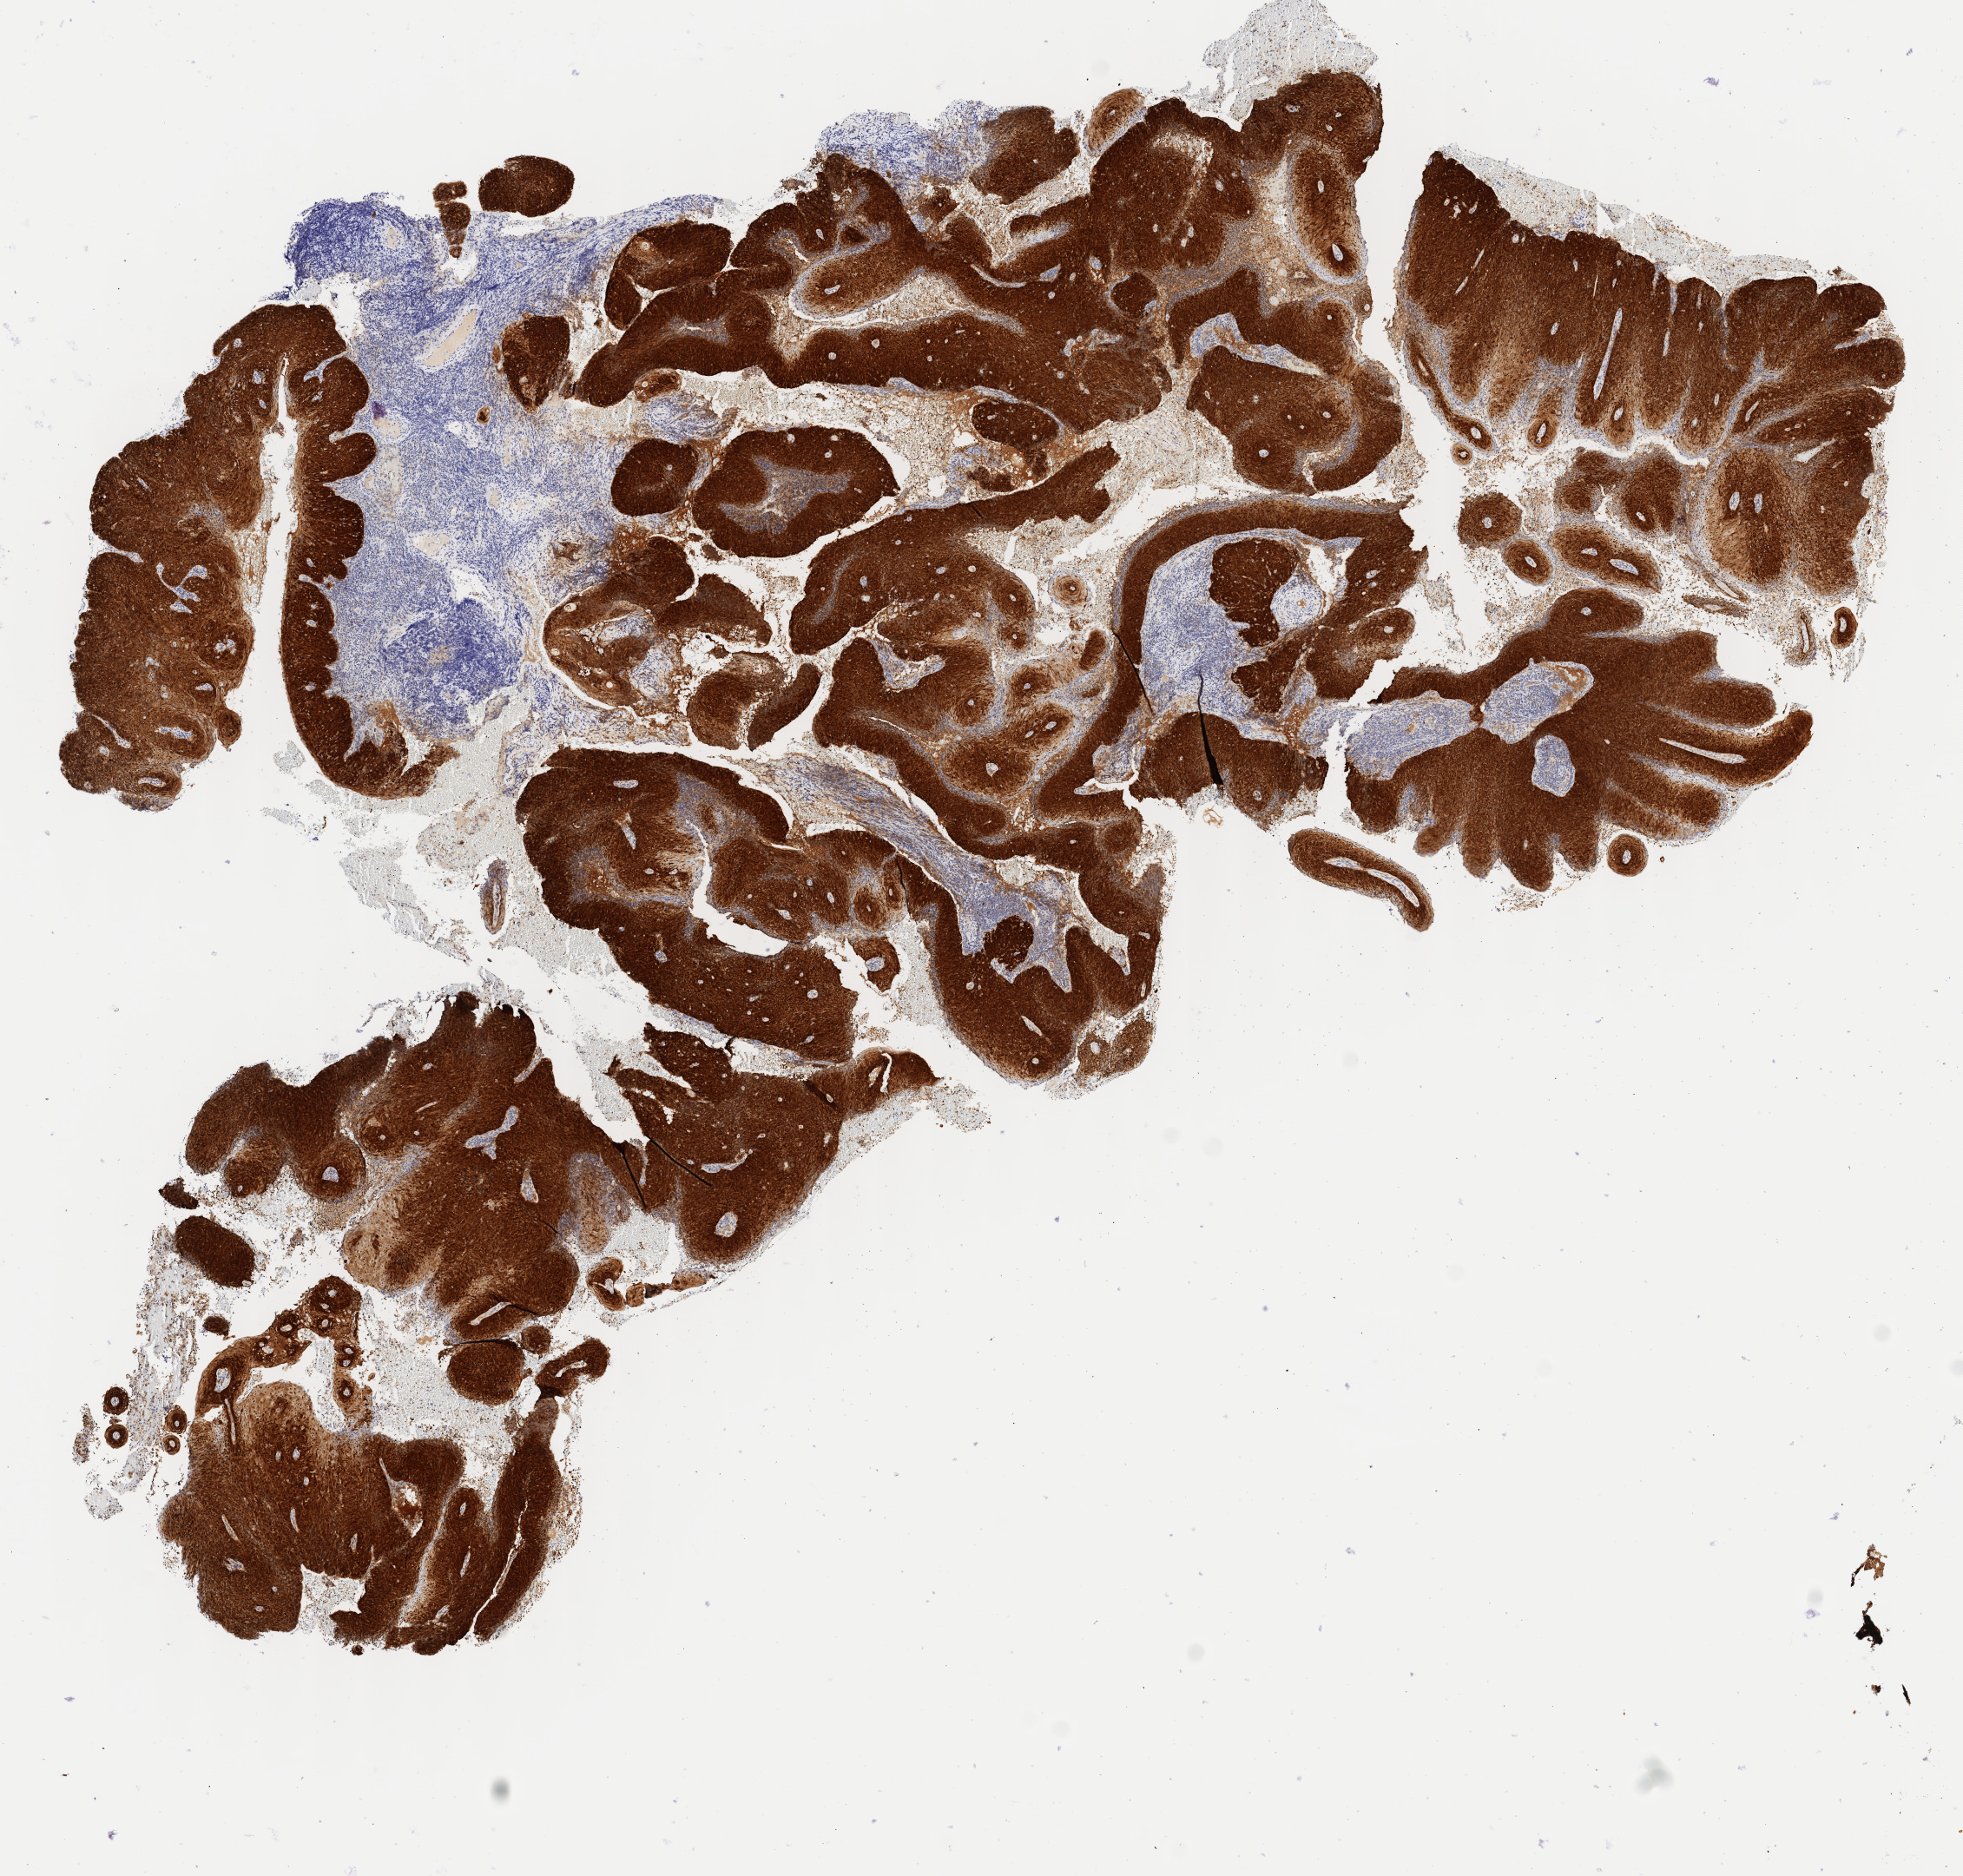
Whole-slide image, immunohistochemical stain for p16 (p16INK4a), a low-resolution overview of the entire scanned area, about 9.0 x 8.6 mm, specimen: tumor tissue, site: cervix. Female patient, 54 years old.
Histologic diagnosis: Squamous cell carcinoma, large cell, nonkeratinizing, NOS.